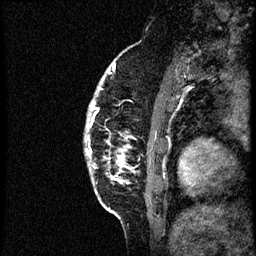
Breast MRI (dynamic contrast-enhanced), one sagittal slice; position 10 of 56 along the scan axis; dynamic contrast-enhanced study with each time point stored as its own series, time point 2 of 3 at this slice position (early post-contrast, ordered by acquisition time); 1.5 T; TE 4.2 ms, TR 21.3 ms; 256 × 256 image matrix, field of view 200 × 200 mm. Female patient, age 41 years. From the clinical record (not read from this slice): setting: breast cancer imaged before/during neoadjuvant chemotherapy; receptor status: HER2-positive.
Structures marked on this image (semi-automatically segmented with operator editing):
- analysis volume of interest (the breast-tissue region the enhancement analysis was run in; not a lesion): bounding box [x1, y1, x2, y2] px = [84, 73, 177, 205]
- tumour enhancement mask (voxels above the 100 % enhancement threshold inside the analysis volume of interest): [88, 105, 123, 179]